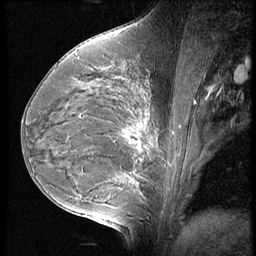
Breast MRI (dynamic contrast-enhanced), one sagittal slice. 3 images stored at this slice position (order not interpretable as contrast timing). 1.5 T. TE 4.2 ms, TR 9 ms. 2.5 mm slice thickness. 256 × 256 image matrix, field of view 180 × 180 mm. Patient: female, 35 years. Case-level facts recorded for this patient, not image findings: setting: breast cancer imaged before/during neoadjuvant chemotherapy; receptor status: HR-positive, HER2-negative.
Outlined on this slice (semi-automatic segmentation, software-assisted and operator-edited):
- analysis volume of interest (the breast-tissue region the enhancement analysis was run in; not a lesion): box from (x=56, y=58) to (x=176, y=202) px
- tumour enhancement mask (voxels above the 140 % enhancement threshold inside the analysis volume of interest): (x=125, y=133)–(x=143, y=152)